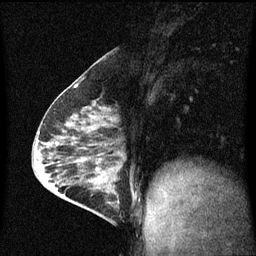
Breast MRI (dynamic contrast-enhanced), one sagittal slice; position 29 of 60 along the scan axis; dynamic contrast-enhanced series, image 2 of 3 at this slice position (ordered by acquisition); 1.5 T; TE 4.2 ms, TR 8 ms; 2 mm slice thickness; 256 × 256 image matrix, field of view 200 × 200 mm. Patient: female, 64 years.
Annotated regions visible in this slice (semi-automatically segmented with operator editing):
- analysis volume of interest (the breast-tissue region the enhancement analysis was run in; not a lesion): bounding box <87,176,121,217> (left, top, right, bottom; pixels)
- tumour enhancement mask (voxels above the 70 % enhancement threshold inside the analysis volume of interest): <93,180,119,203>